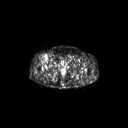
FDG PET of an extremity soft-tissue mass (from a PET/CT study), one axial slice; slice 309 of 311 in the series (ordered by position); 3.27 mm slice thickness; 128 × 128 image matrix, field of view 700 × 700 mm. Patient: male, 56 years. Case-level facts recorded for this patient, not image findings: histological type: pleiomorphic leiomyosarcoma; grade: intermediate; site of the primary tumour: right thigh.
Annotated regions visible in this slice (expert contour drawn on MRI and transferred to this co-registered scan by the dataset authors):
- gross tumour volume including surrounding oedema: box from (x=43, y=55) to (x=48, y=60) px